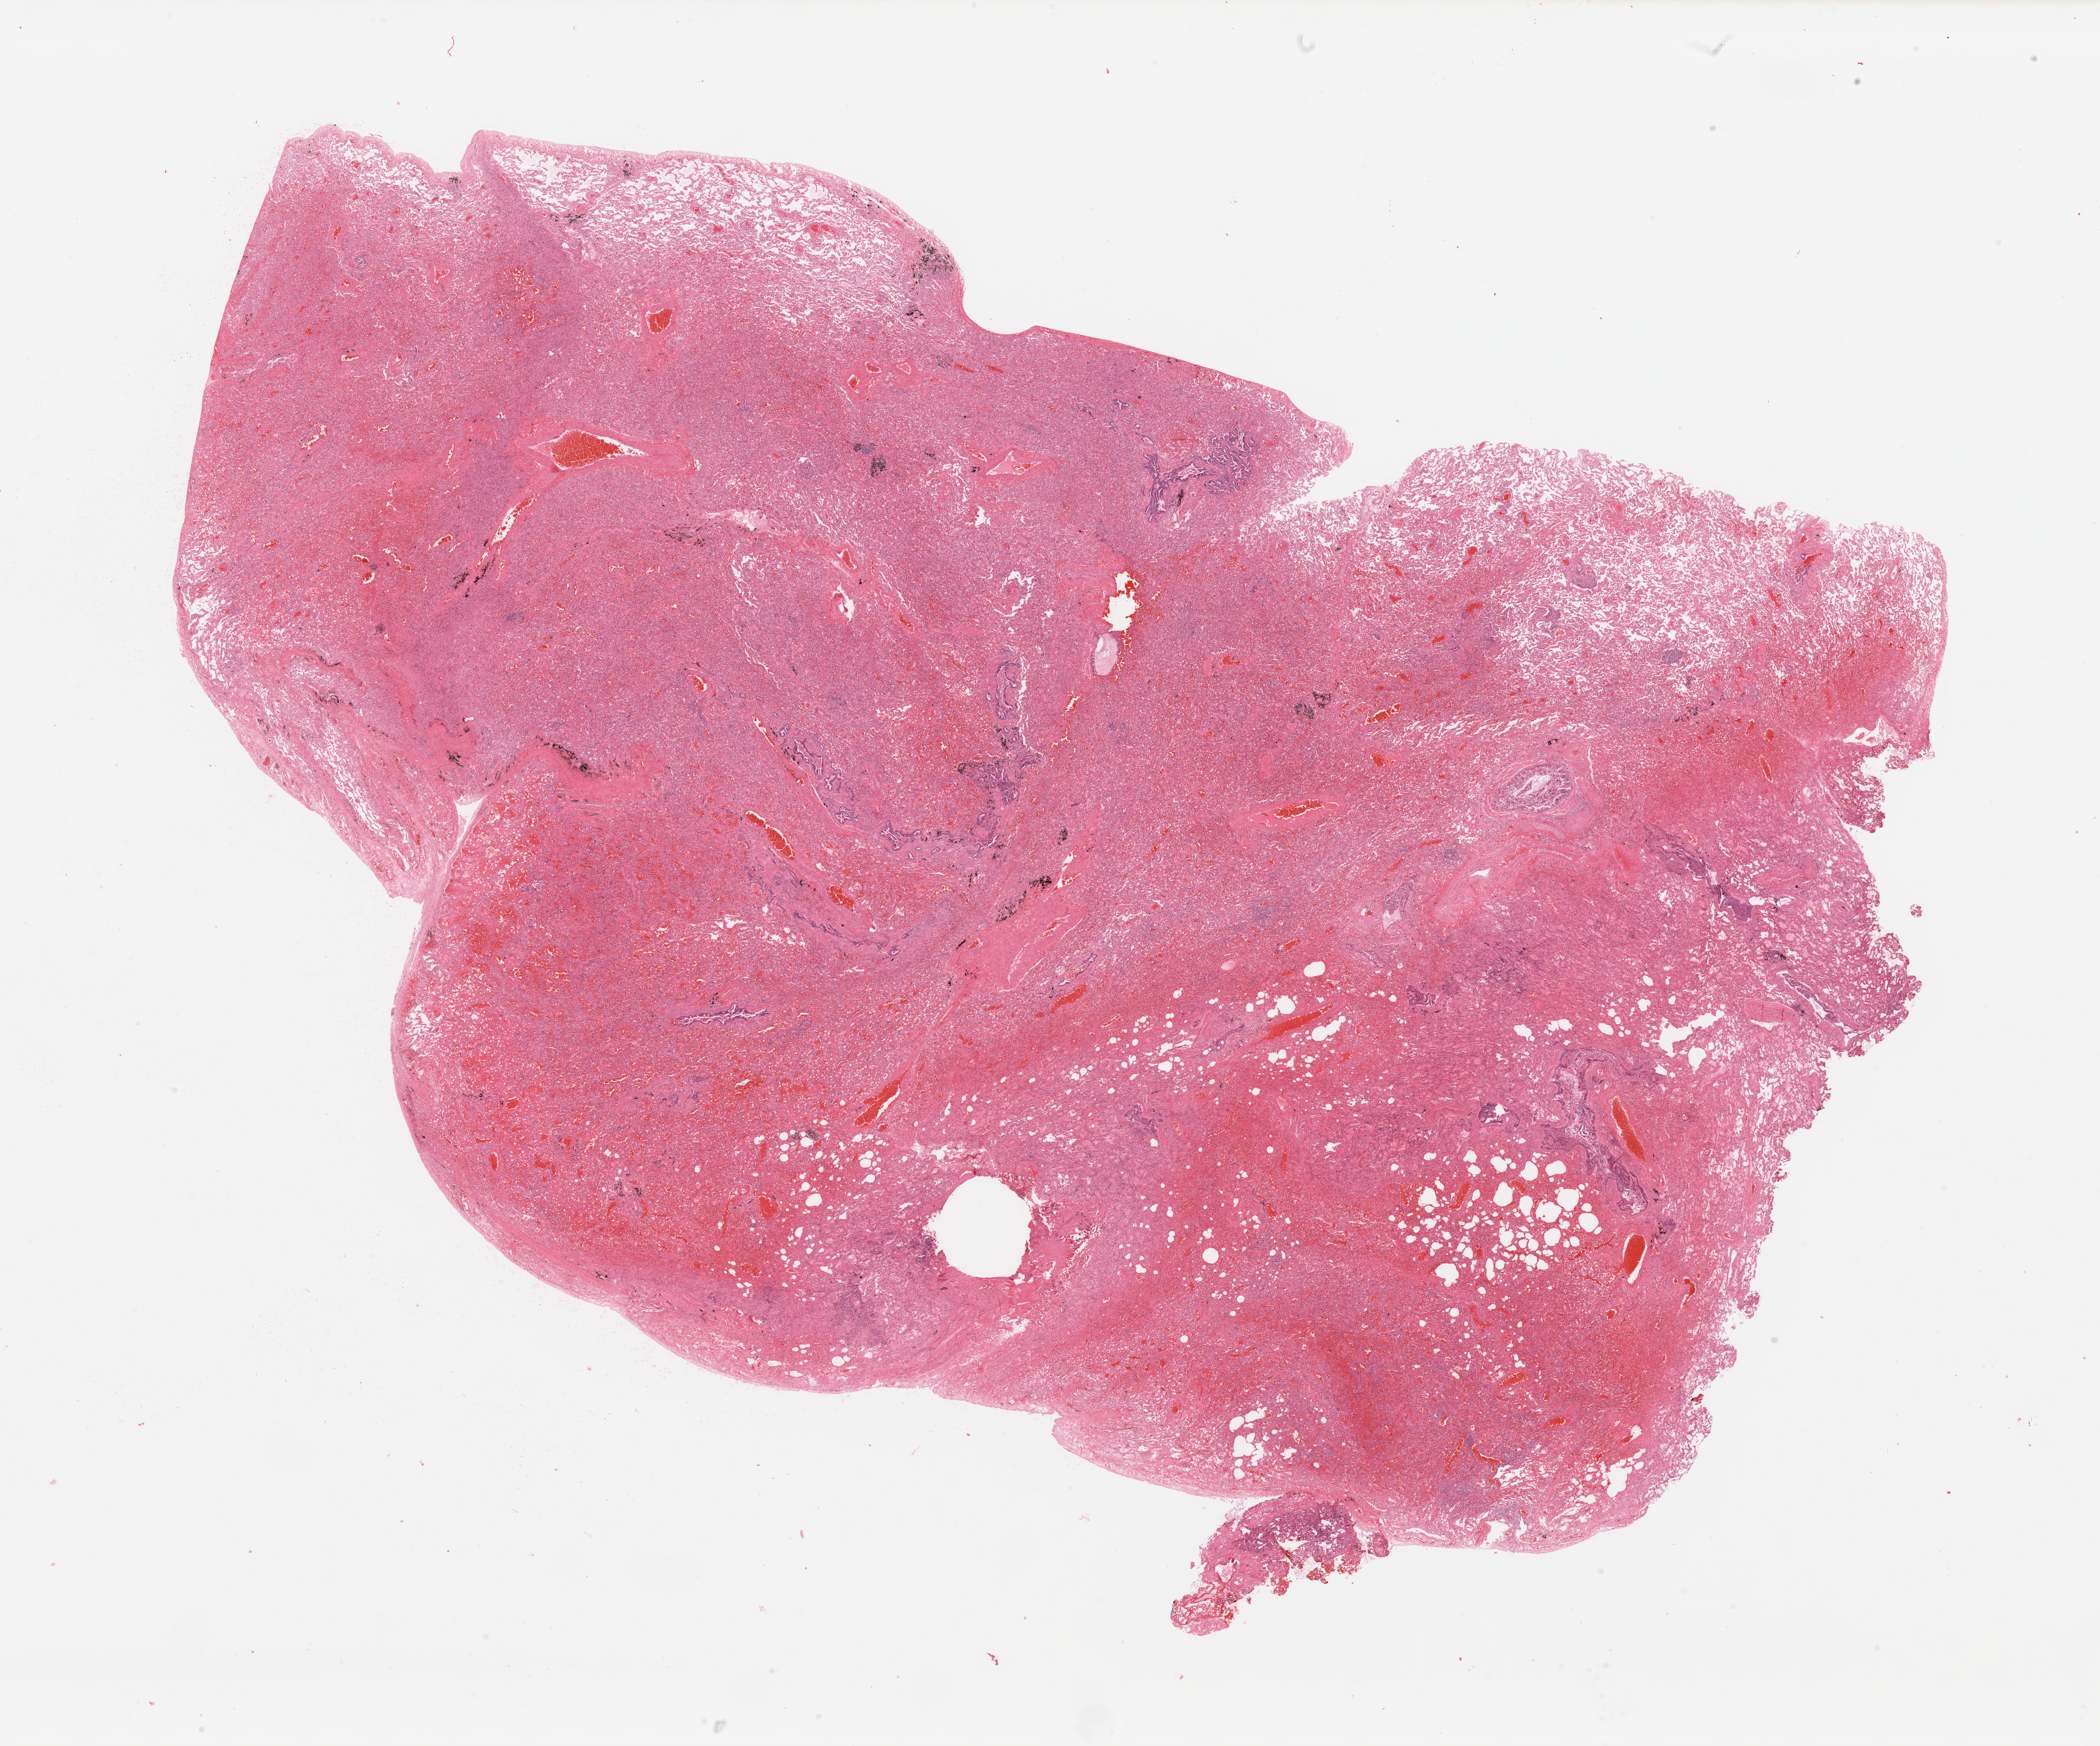
Digitized Hematoxylin and eosin (H&E) stained tissue section (whole slide), shown as a low-resolution overview of the whole scanned area (about 27.6 x 22.9 mm, slide scanned at 20x). Normal (non-tumour) tissue sample, sampled site: lung. Patient: female, age 47 years.
This section: normal (non-tumour) tissue from the same patient. Patient diagnosis: Adenocarcinoma, NOS.